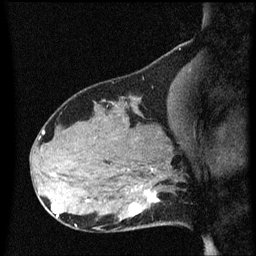
Breast MRI (dynamic contrast-enhanced), one sagittal slice. Position 23 of 60 along the scan axis. Dynamic contrast-enhanced series, image 2 of 3 at this slice position (ordered by acquisition). 1.5 T. TE 4.2 ms, TR 8.4 ms. 2 mm slice thickness. 256 × 256 image matrix. Female patient, age 31 years. Case-level facts recorded for this patient, not image findings: setting: breast cancer imaged before/during neoadjuvant chemotherapy; receptor status: HR-positive, HER2-negative.
Structures marked on this image (semi-automatically segmented with operator editing):
- analysis volume of interest (the breast-tissue region the enhancement analysis was run in; not a lesion): bounding box (x1, y1, x2, y2) in pixels: (102, 166, 176, 229)
- tumour enhancement mask (voxels above the 70 % enhancement threshold inside the analysis volume of interest): (130, 192, 158, 215)